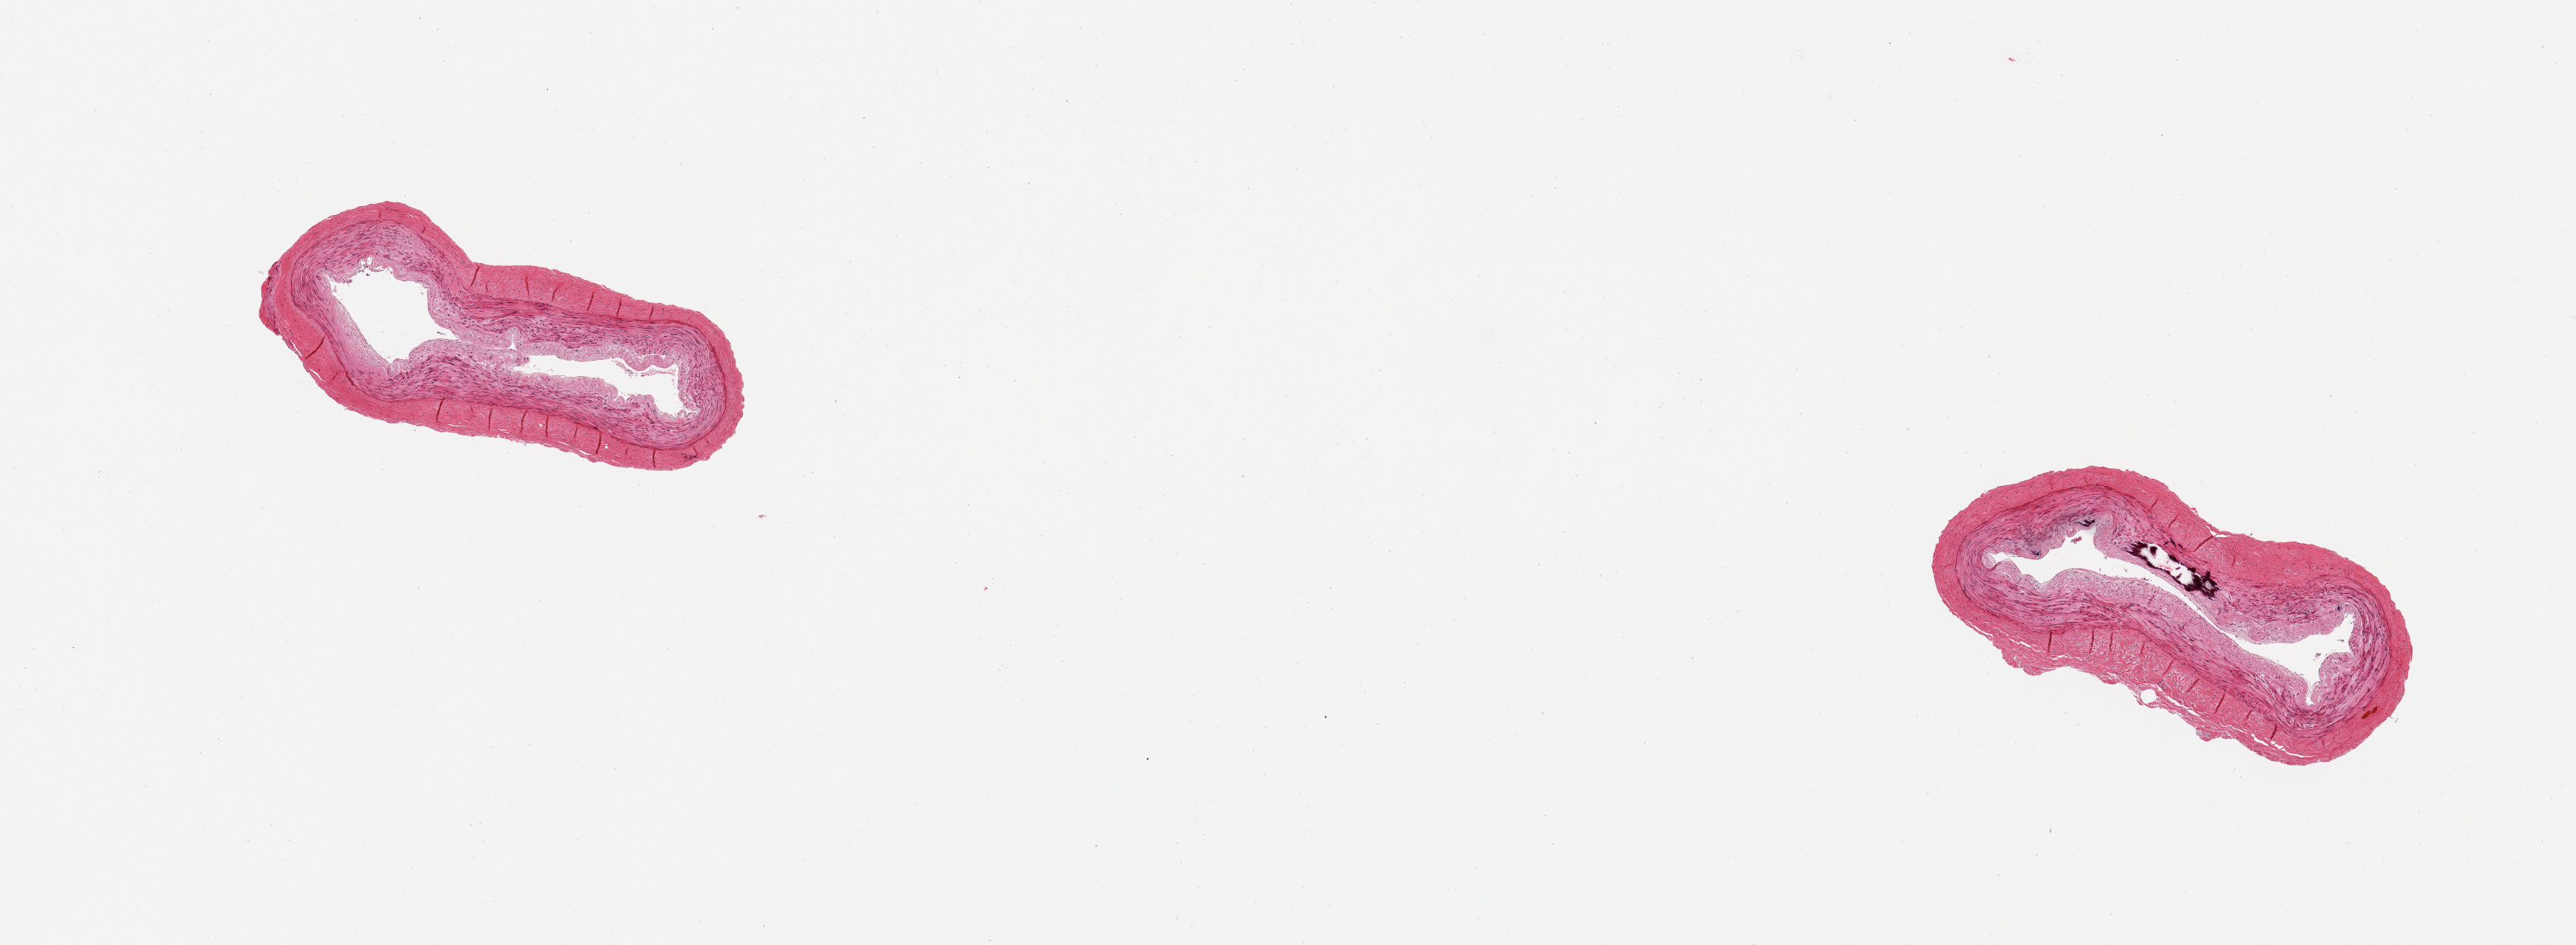
Digitized hematoxylin and eosin (H&E)-stained section, shown as a low-resolution overview of the whole scanned area (about 13.8 x 5.1 mm). PAXgene-fixed, paraffin-embedded tissue. Target tissue: tibial artery. Donor tissue sample. Female donor.
Review note (as recorded): 2 pieces; medial calcification in one piece.